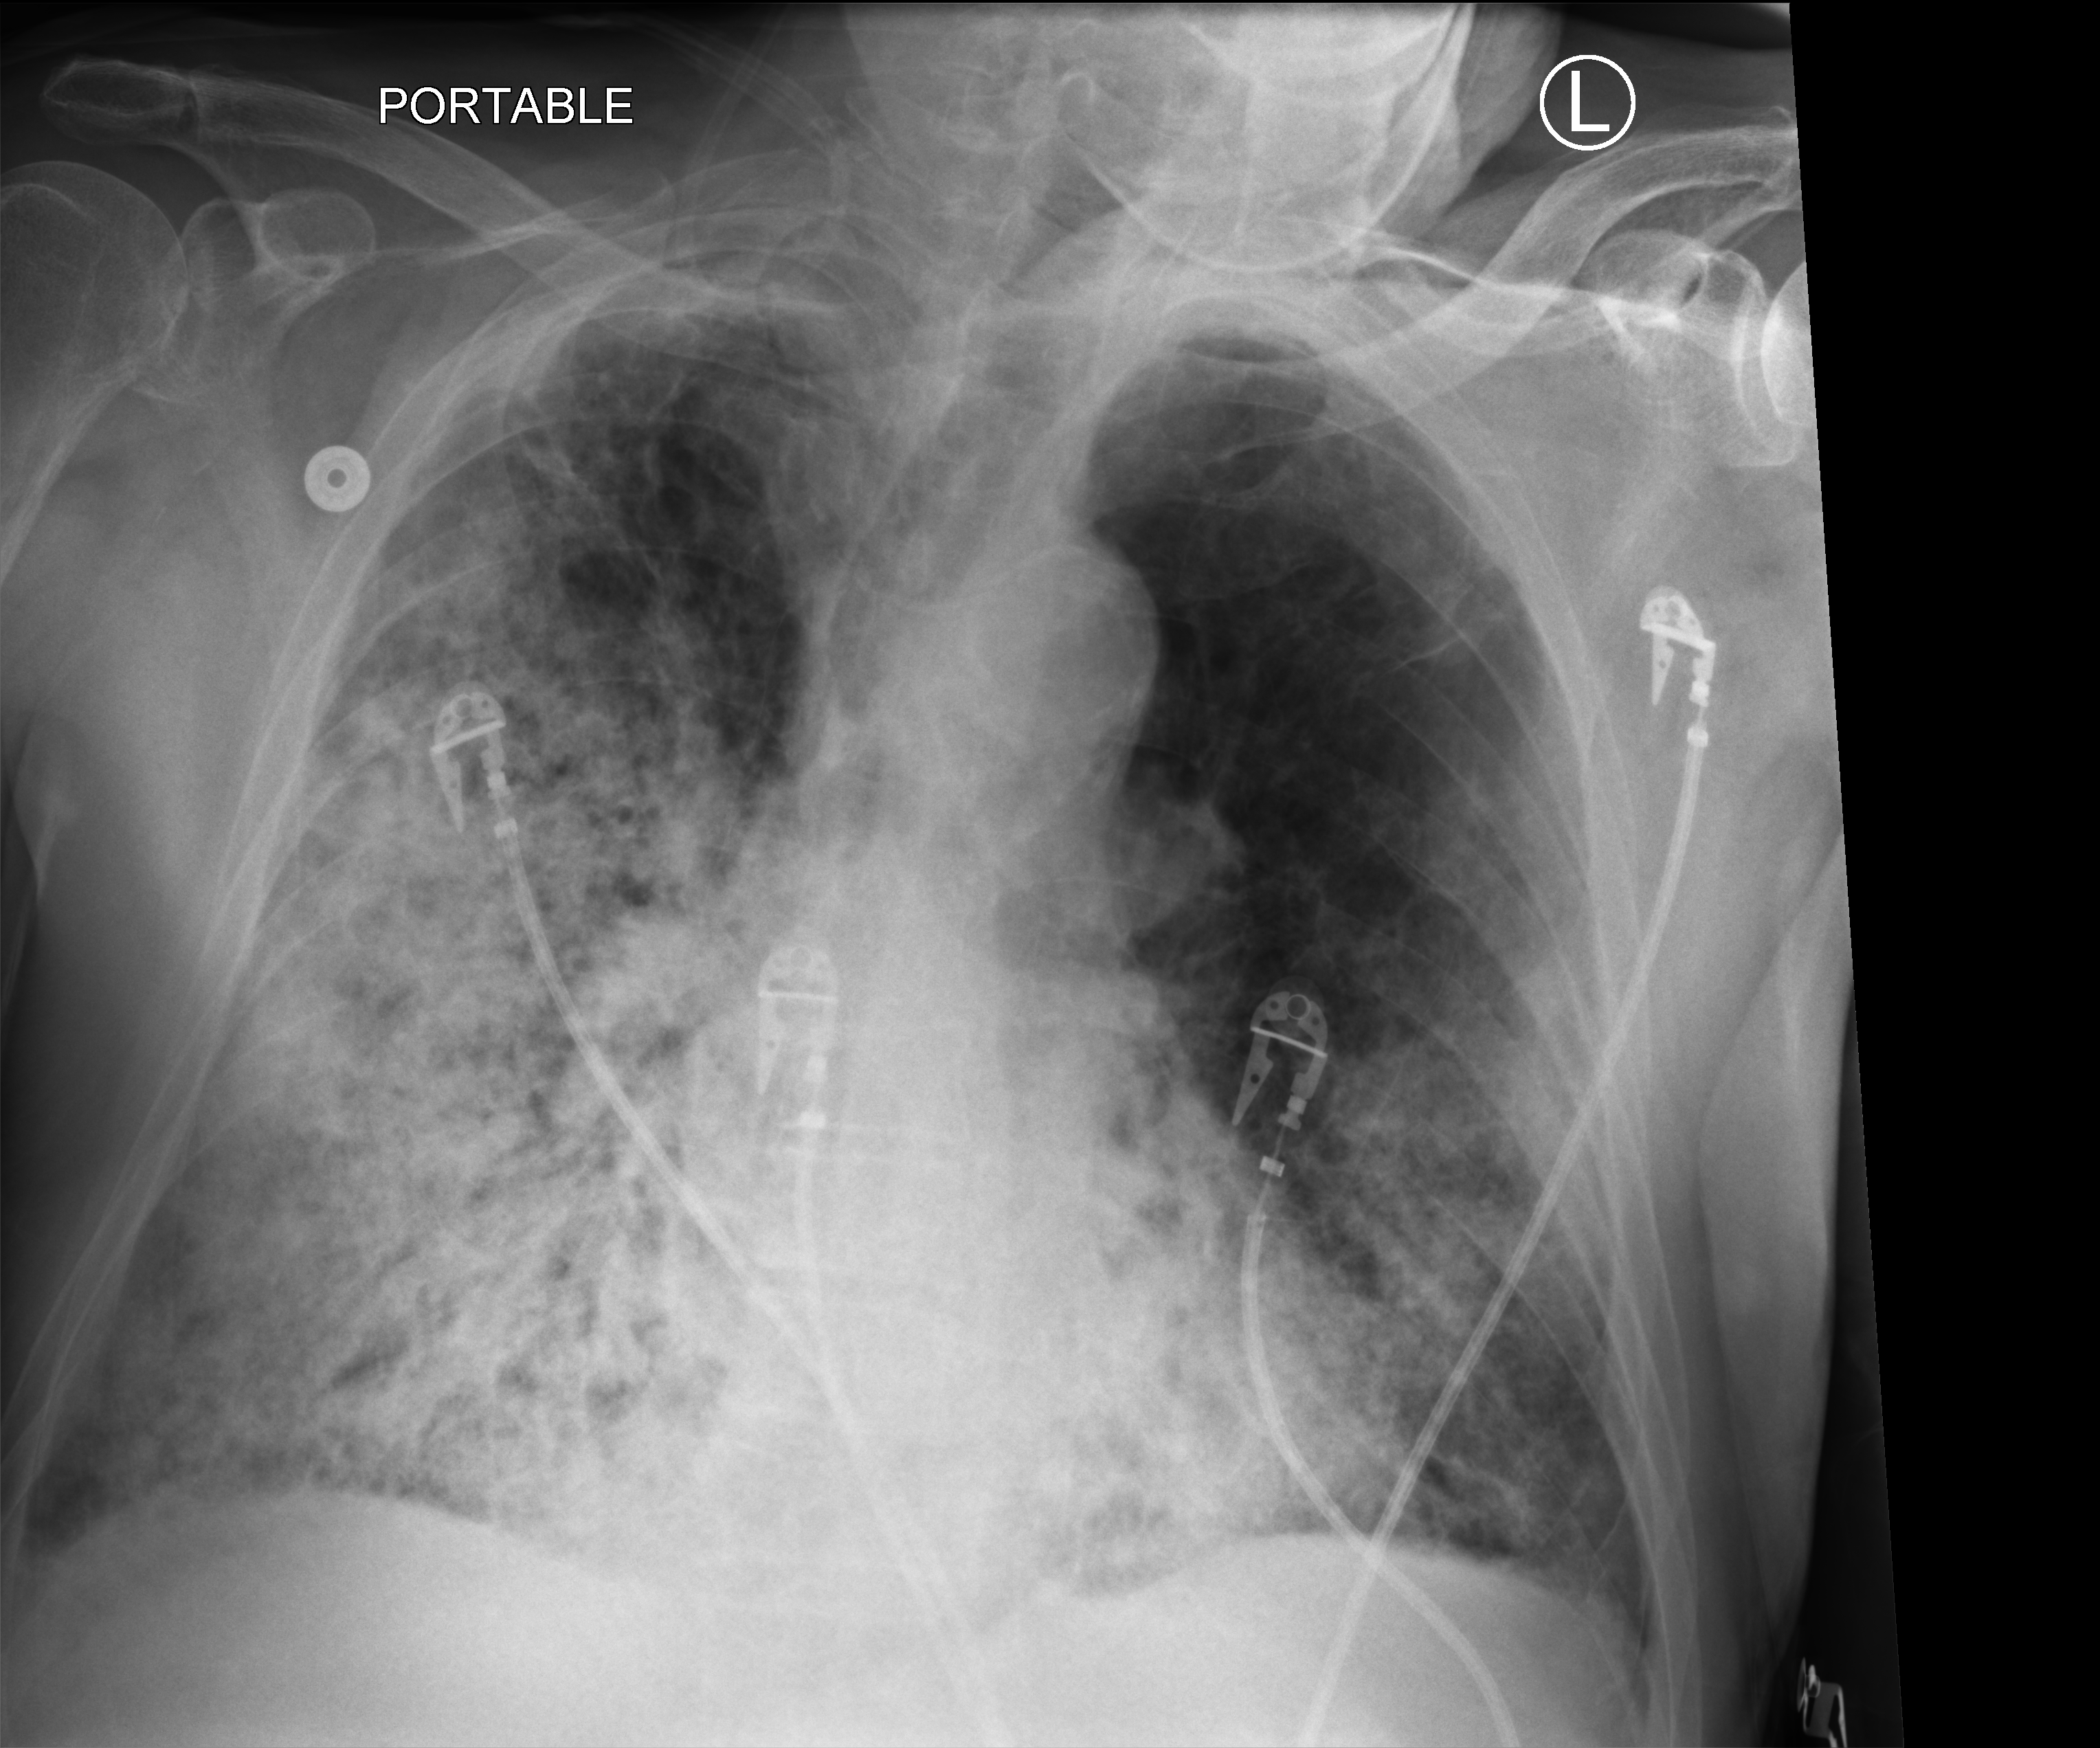
Portable chest radiograph, anteroposterior (AP) projection. Patient hospitalised with COVID-19; male, aged 75–90 years.
Admission-level facts for this patient (not findings on this image; timing relative to this image not recorded): chronic kidney disease (admission record): yes; mechanically ventilated during this hospital stay: no; admitted to intensive care during this hospital stay: no.